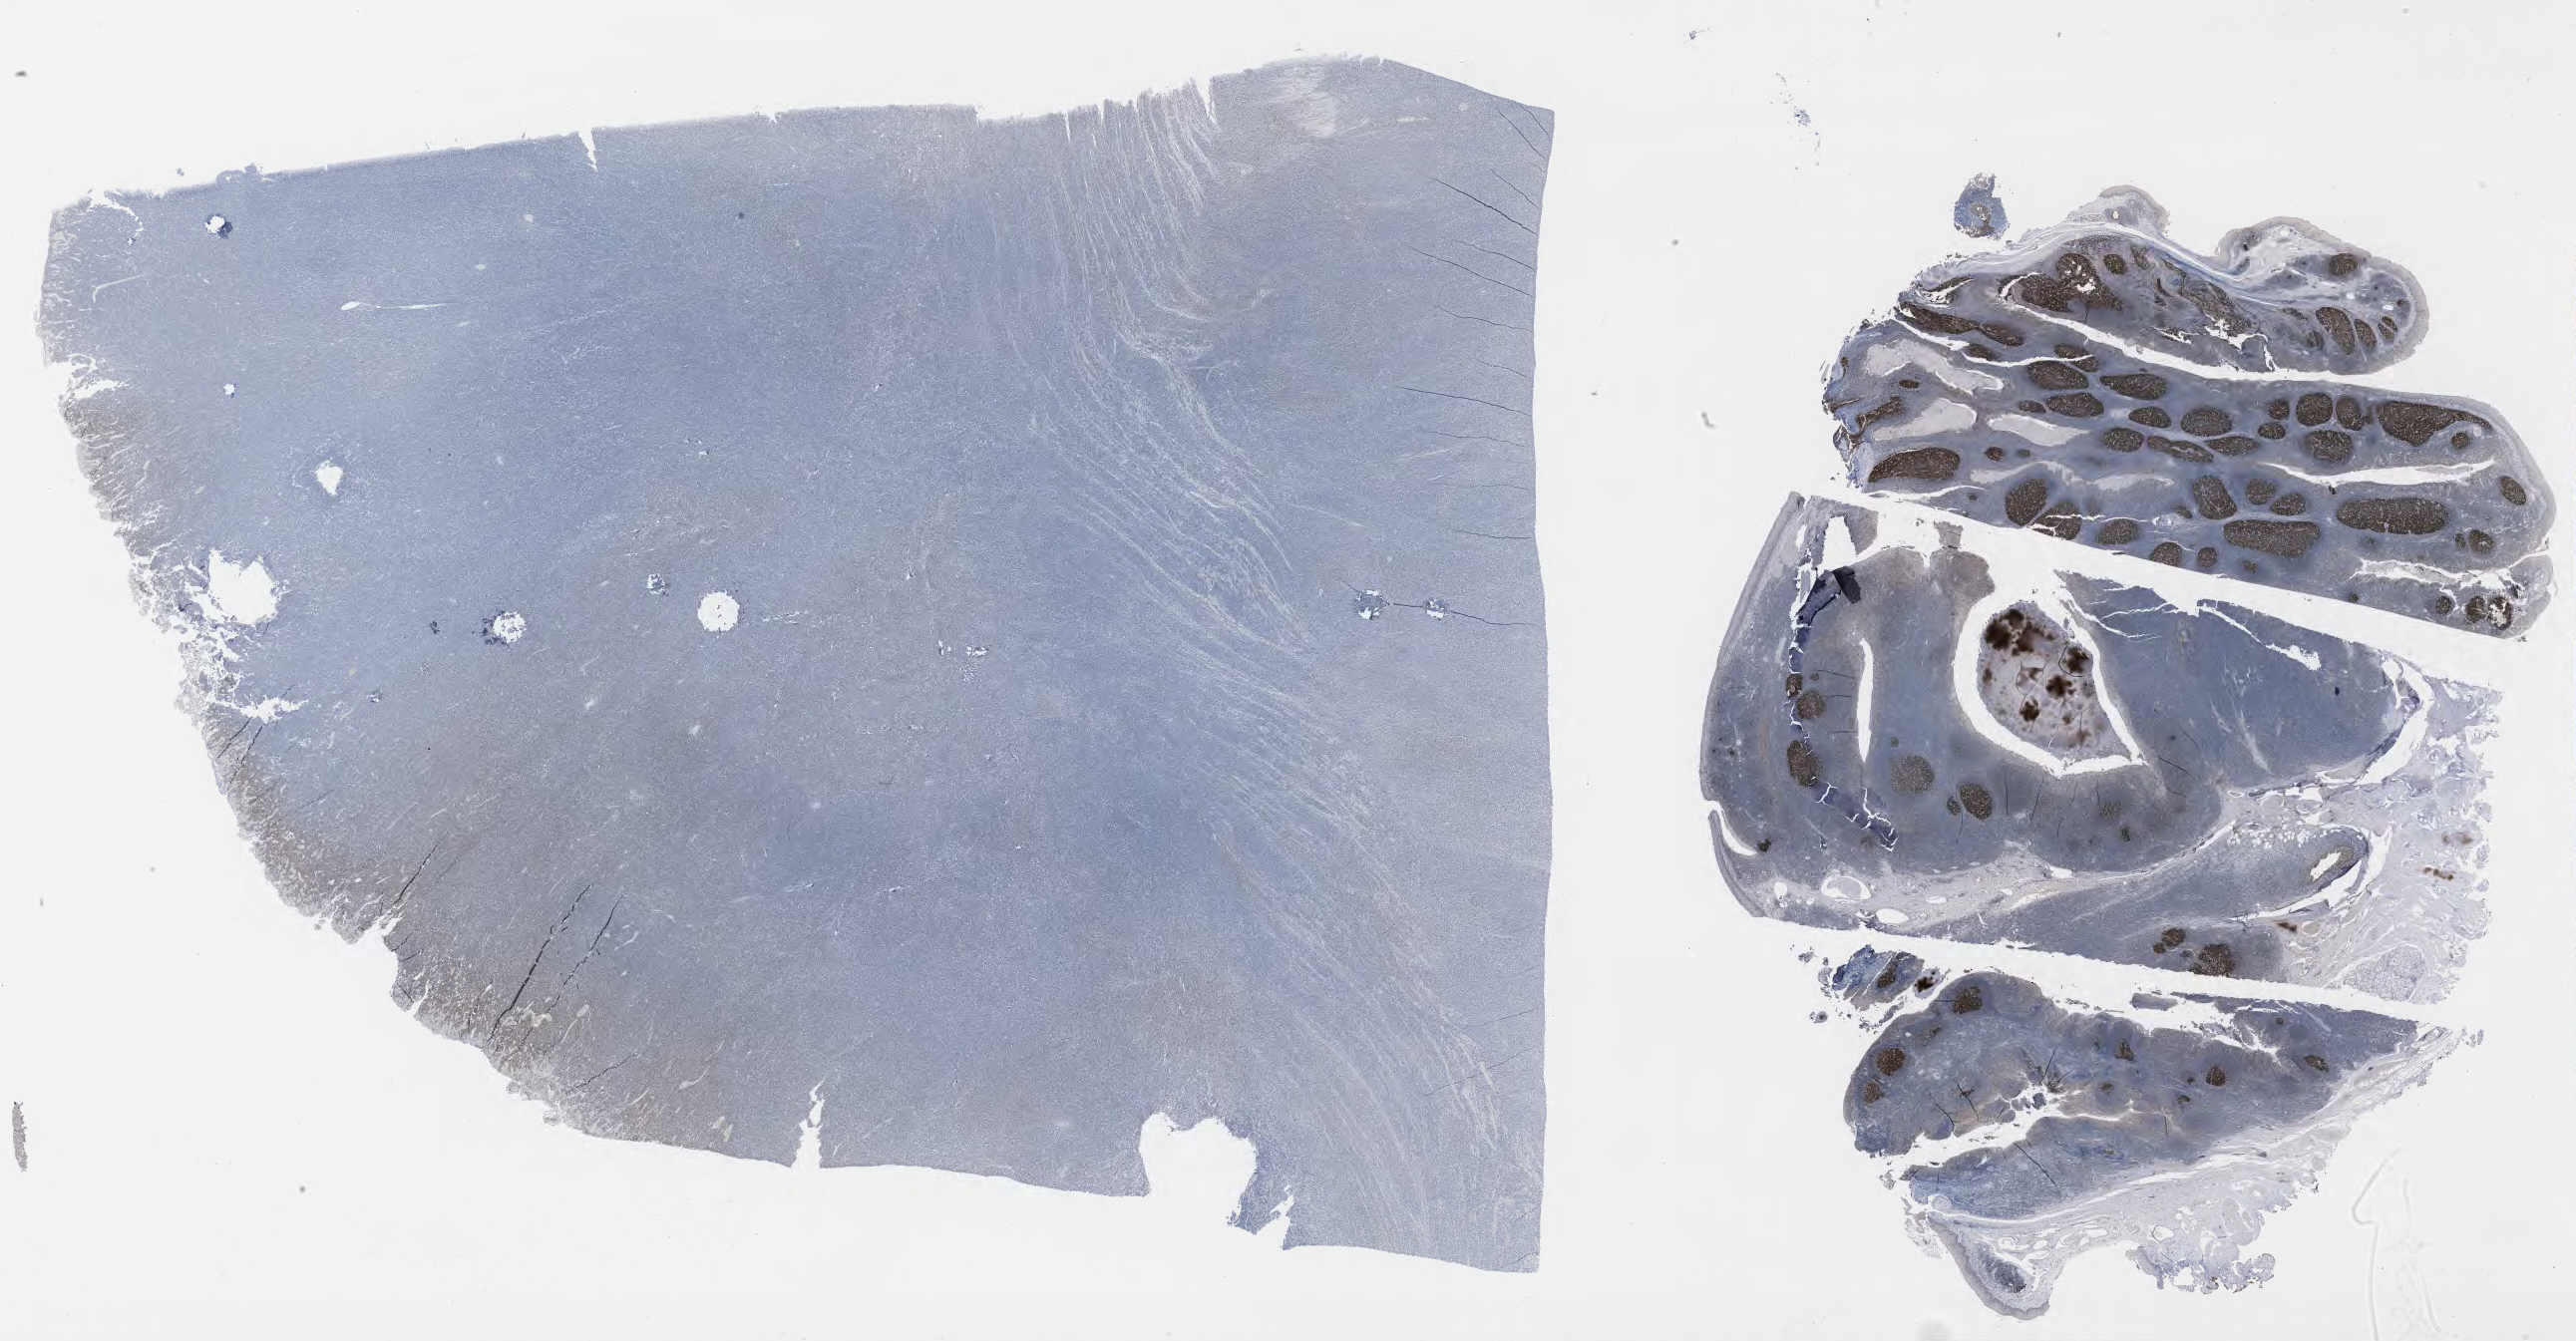
Immunohistochemistry (IHC) whole-slide image stained for BCL6 — shown as a low-resolution overview of the whole scanned area (about 41.7 x 21.7 mm). Specimen: tumor tissue. Patient male; age 17 years.
Histologic diagnosis: Burkitt lymphoma, NOS.